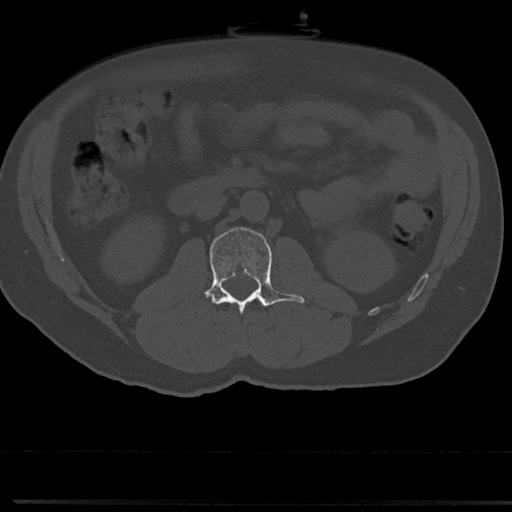
CT including the spine, one axial slice; slice 16 of 817 in the series (ordered by position); reconstruction kernel Br40s/3; 120 kVp; bone window (W 1800 / L 400 HU); 0.5 mm slice thickness; 512 × 512 image matrix, field of view 355 × 355 mm. Patient: male, 61 years. From the clinical record (not read from this slice): primary cancer: prostate.
Outlined on this slice (semi-automatic segmentation, software-assisted and operator-edited):
- L2 vertebra: box from (x=204, y=227) to (x=304, y=313) px